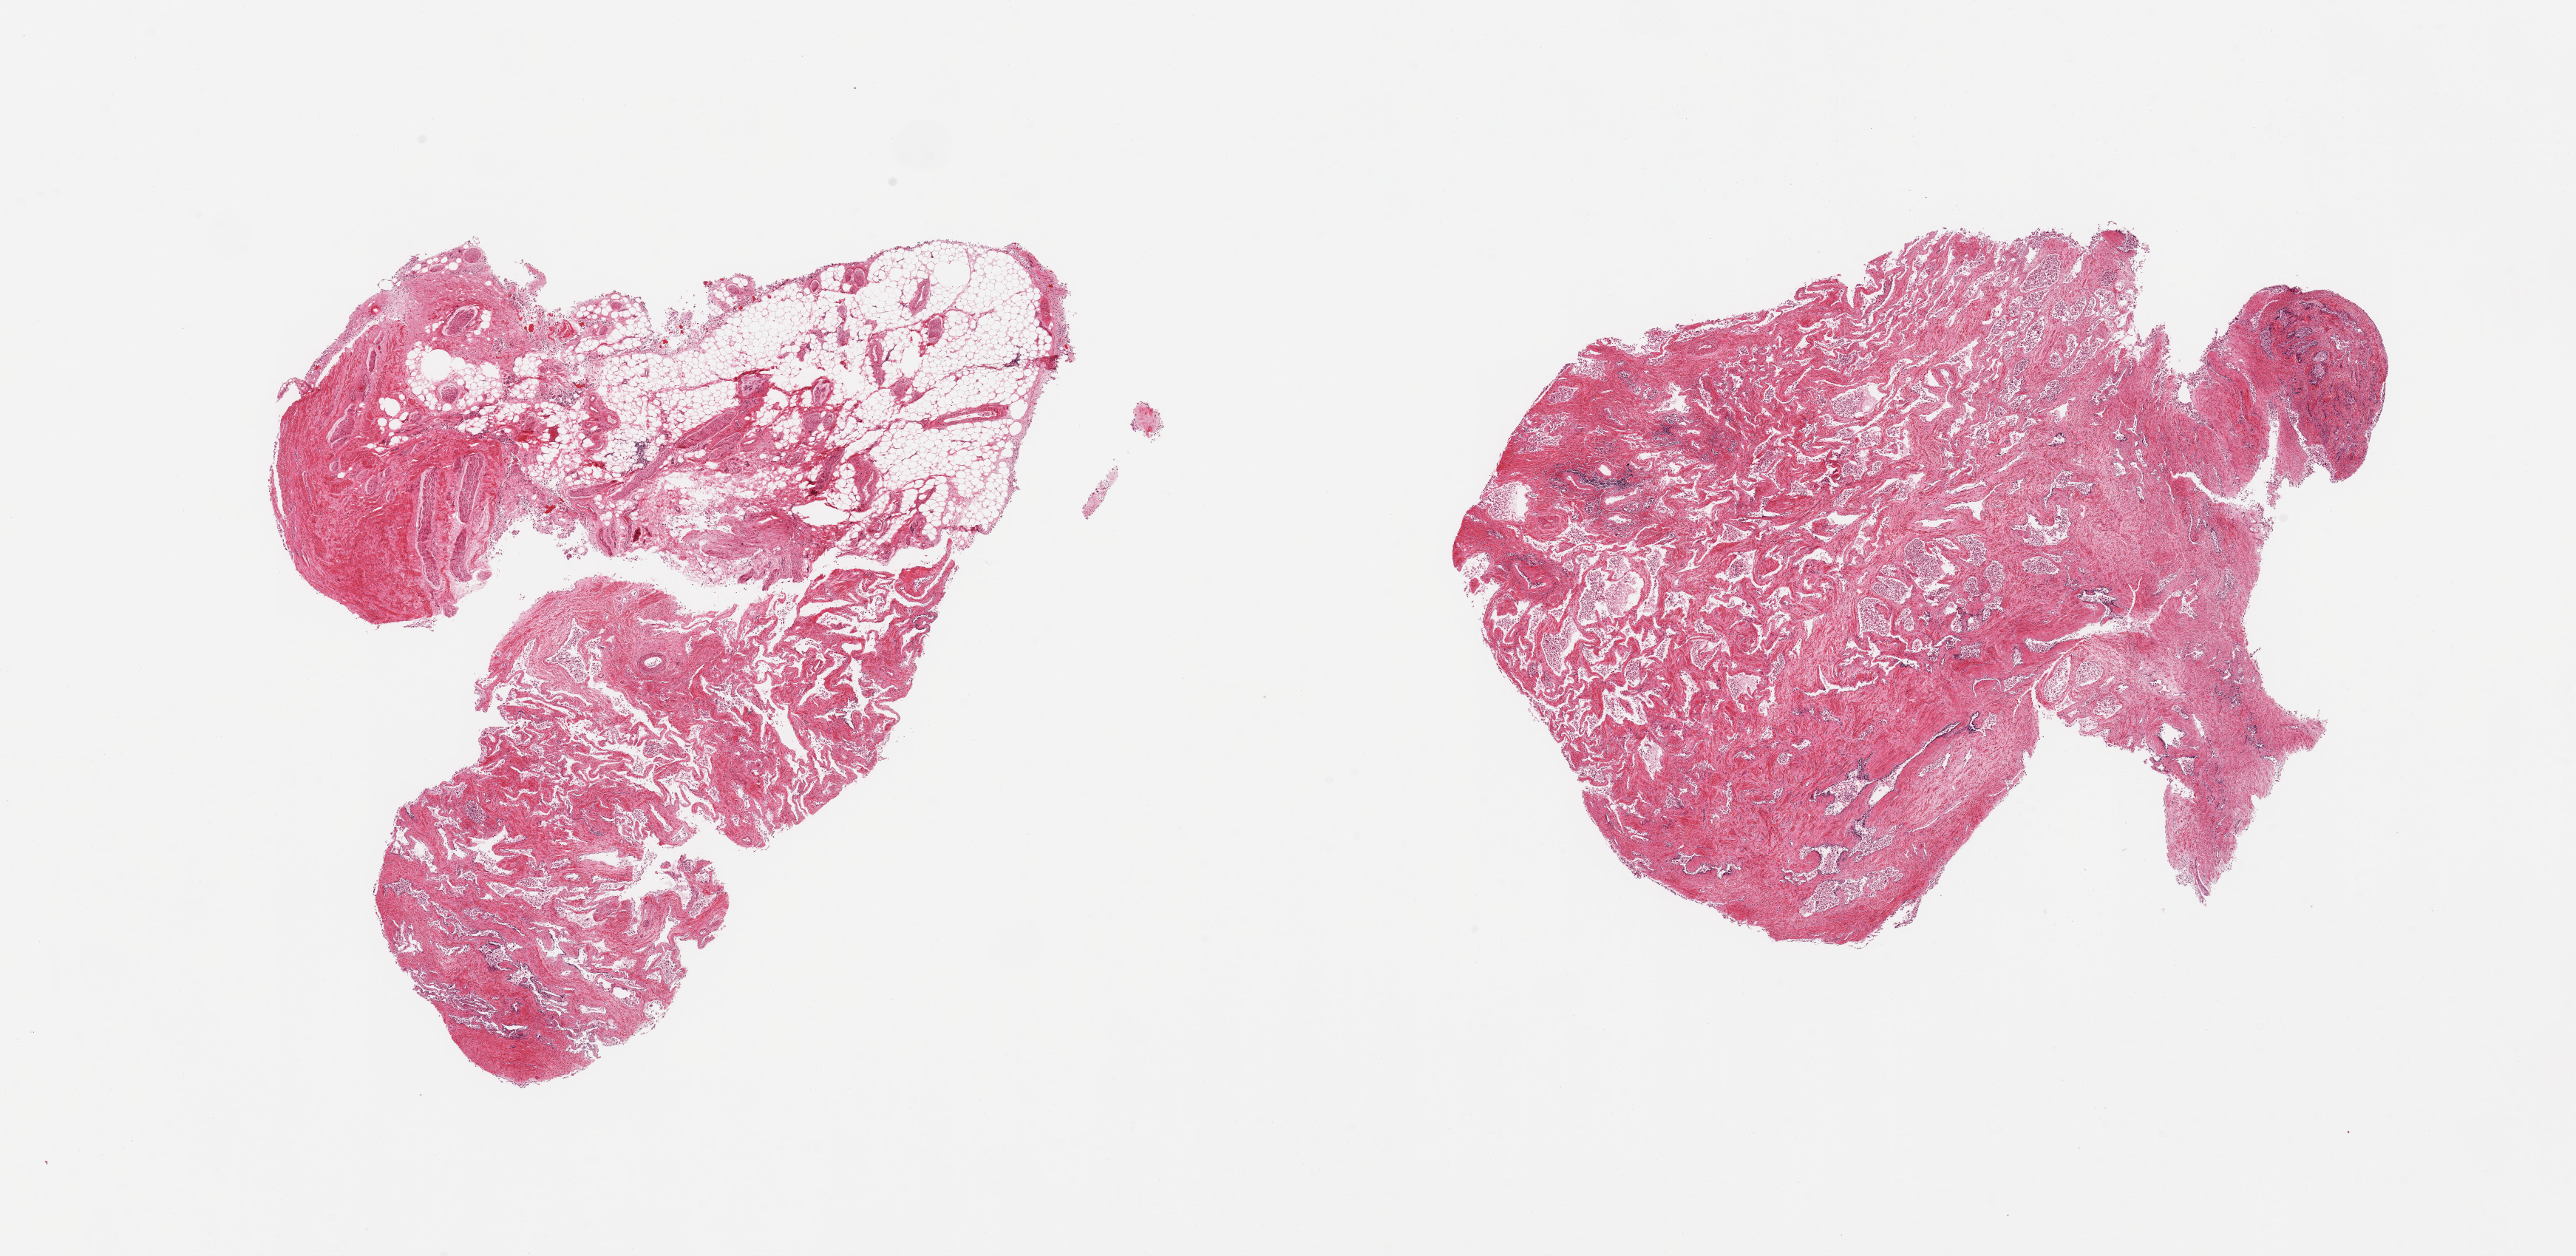
Digitized H&E-stained section, shown as a low-resolution overview of the whole scanned area (about 27.6 x 13.4 mm, from a 20x scan), PAXgene-fixed paraffin-embedded (PFPE) section, sampled site (target tissue): prostate, donor tissue sample. Male donor.
Review note (as recorded): 2 pieces; fibromuscular stroma, glandular lining sloughed, 1 piece is 50% fat and nerve.